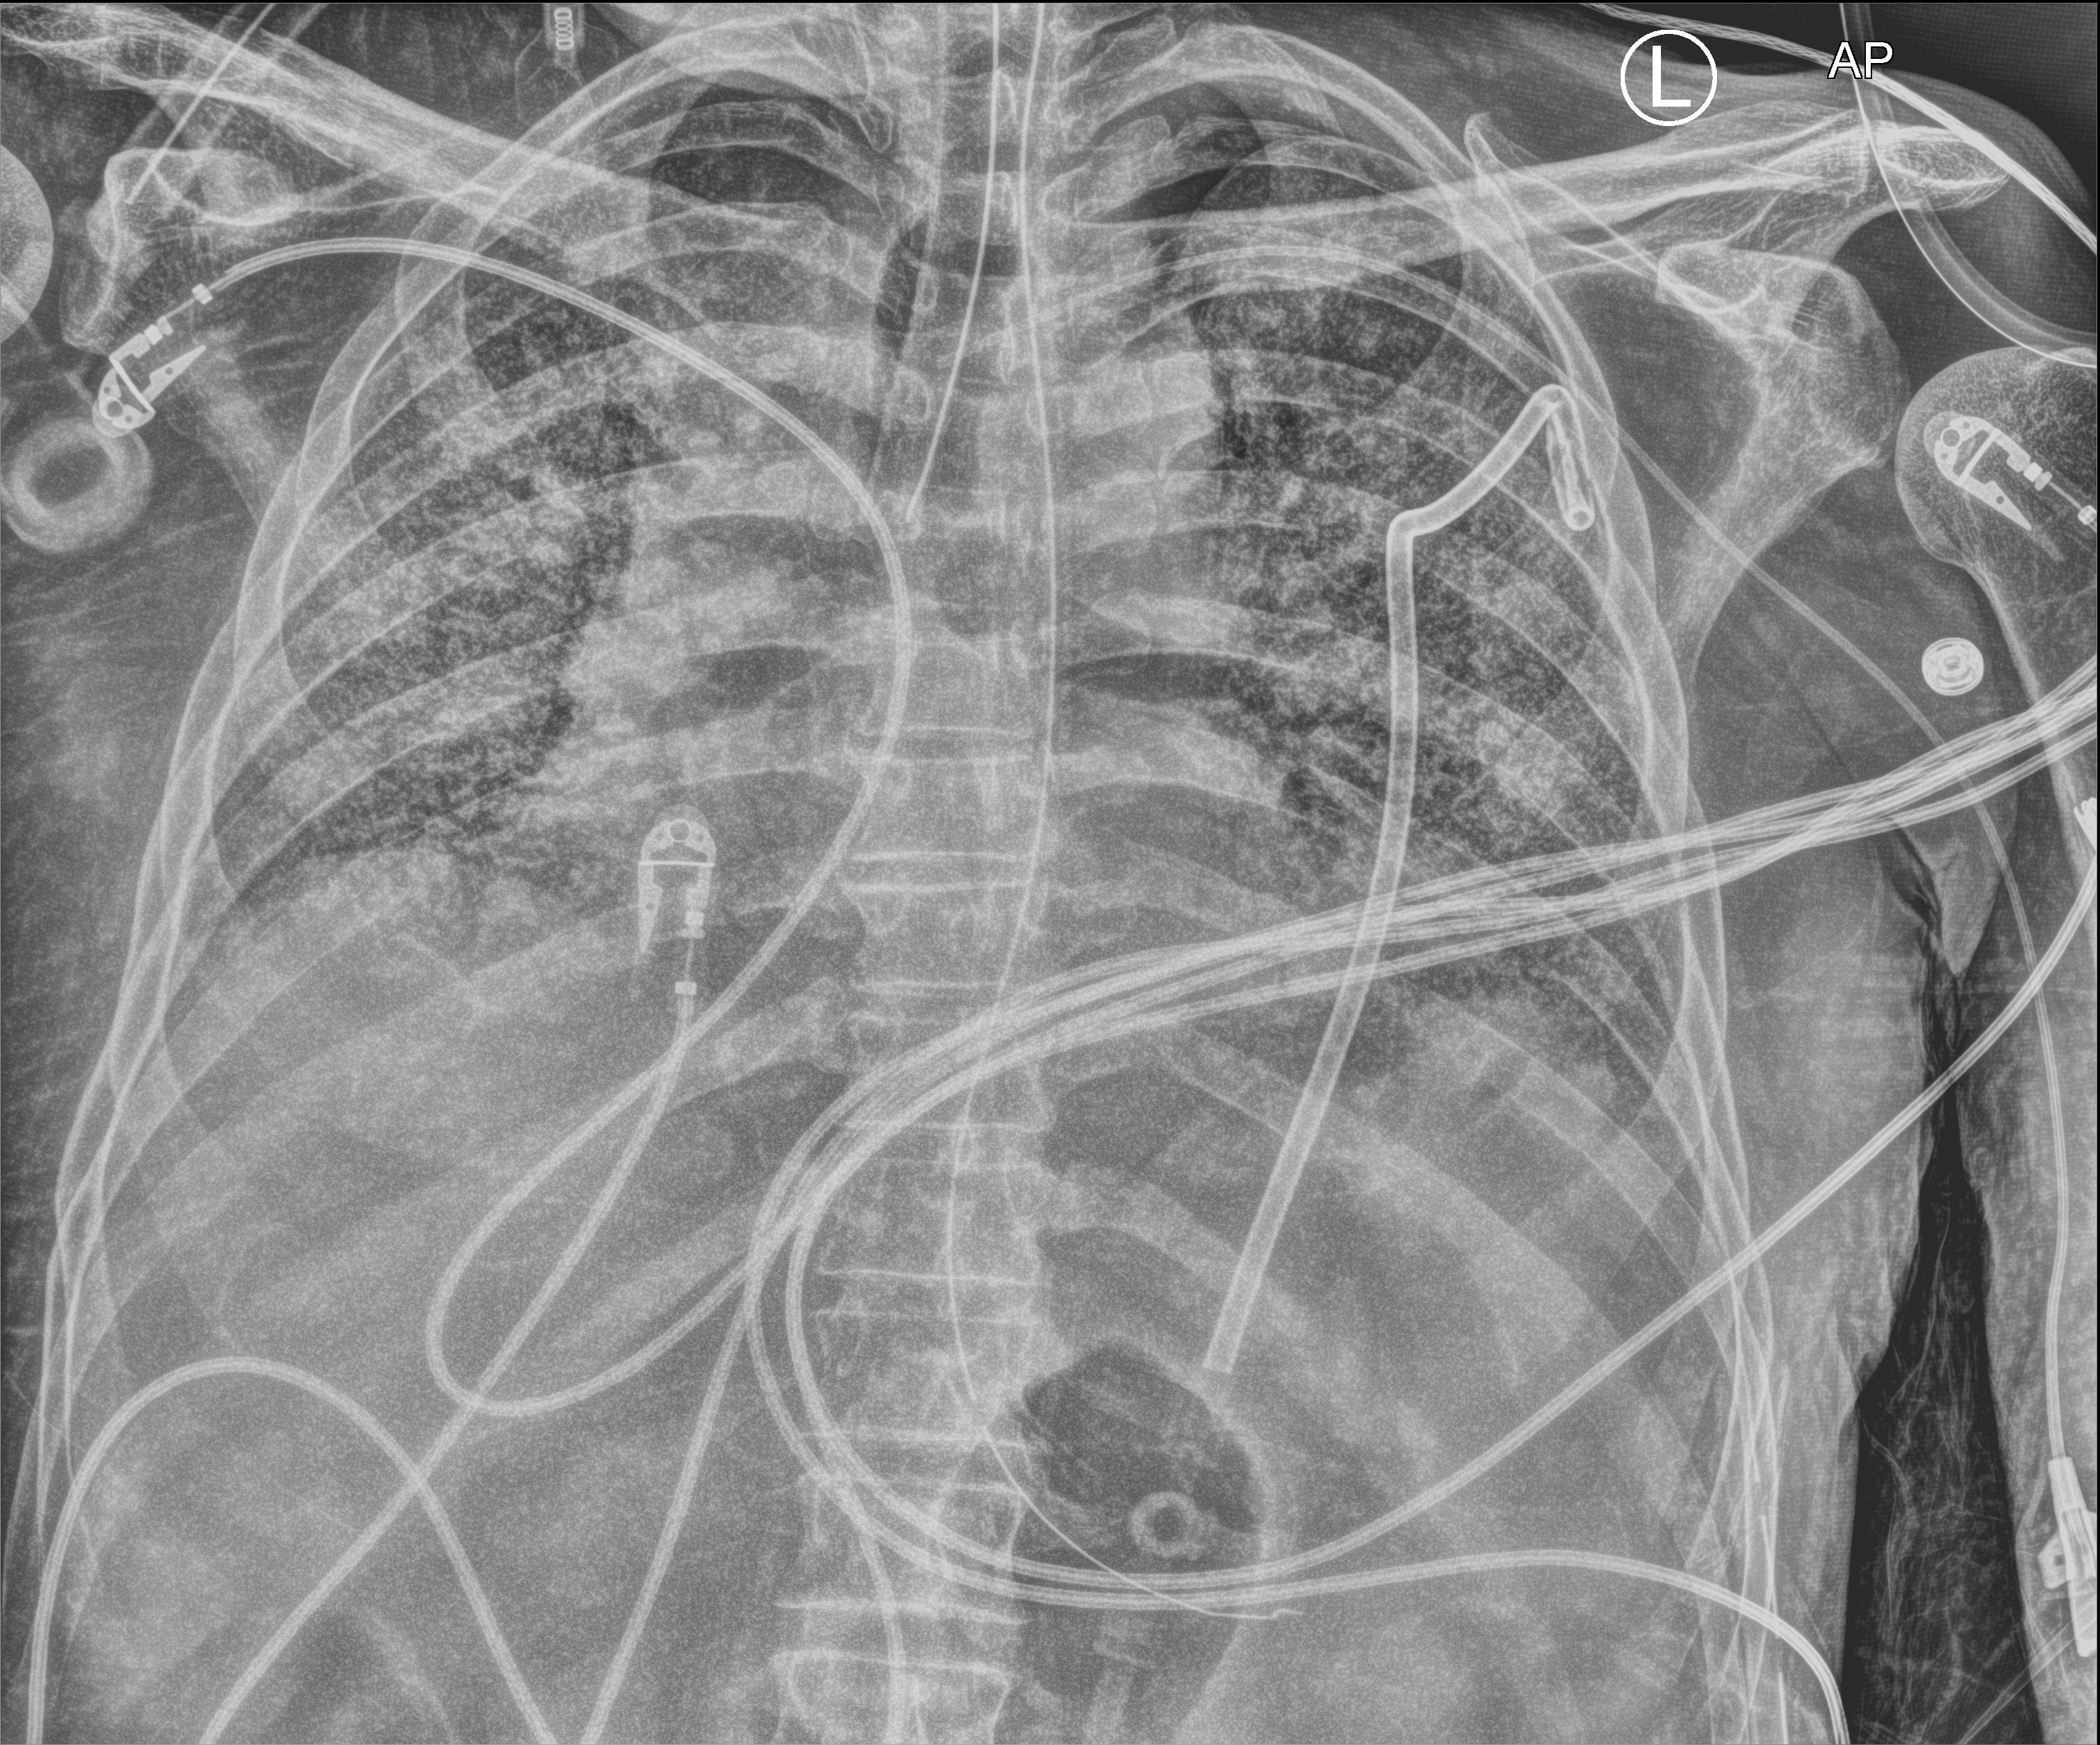
Portable chest radiograph; anteroposterior (AP) projection. Patient hospitalised with COVID-19; male, aged 60–74 years.
Hospital-stay facts (about this admission, not read from this image; timing relative to this image not recorded): mechanically ventilated during this hospital stay: yes.